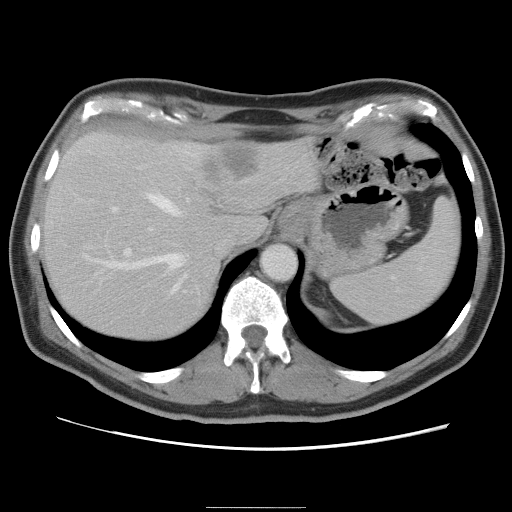
Contrast-enhanced abdominal CT, one axial slice; position 63 of 87 along the scan axis; 120 kVp; intravenous contrast given; soft-tissue window (W 400 / L 40 HU); 512 × 512 image matrix. Male patient, age 63 years. From the clinical record (not read from this slice): diagnosis: colorectal cancer liver metastases, imaged before liver resection; multiple liver metastases: no; largest metastasis: 9 cm.
Outlined on this slice (outlined manually by an expert reader):
- hepatic veins: bounding box [x1, y1, x2, y2] px = [96, 190, 188, 295]
- liver: [40, 131, 317, 342]
- planned liver remnant (the part of the liver to remain after resection): [41, 159, 220, 342]
- portal vein (with intrahepatic branches): [101, 206, 186, 292]
- liver metastasis: [206, 144, 257, 186]